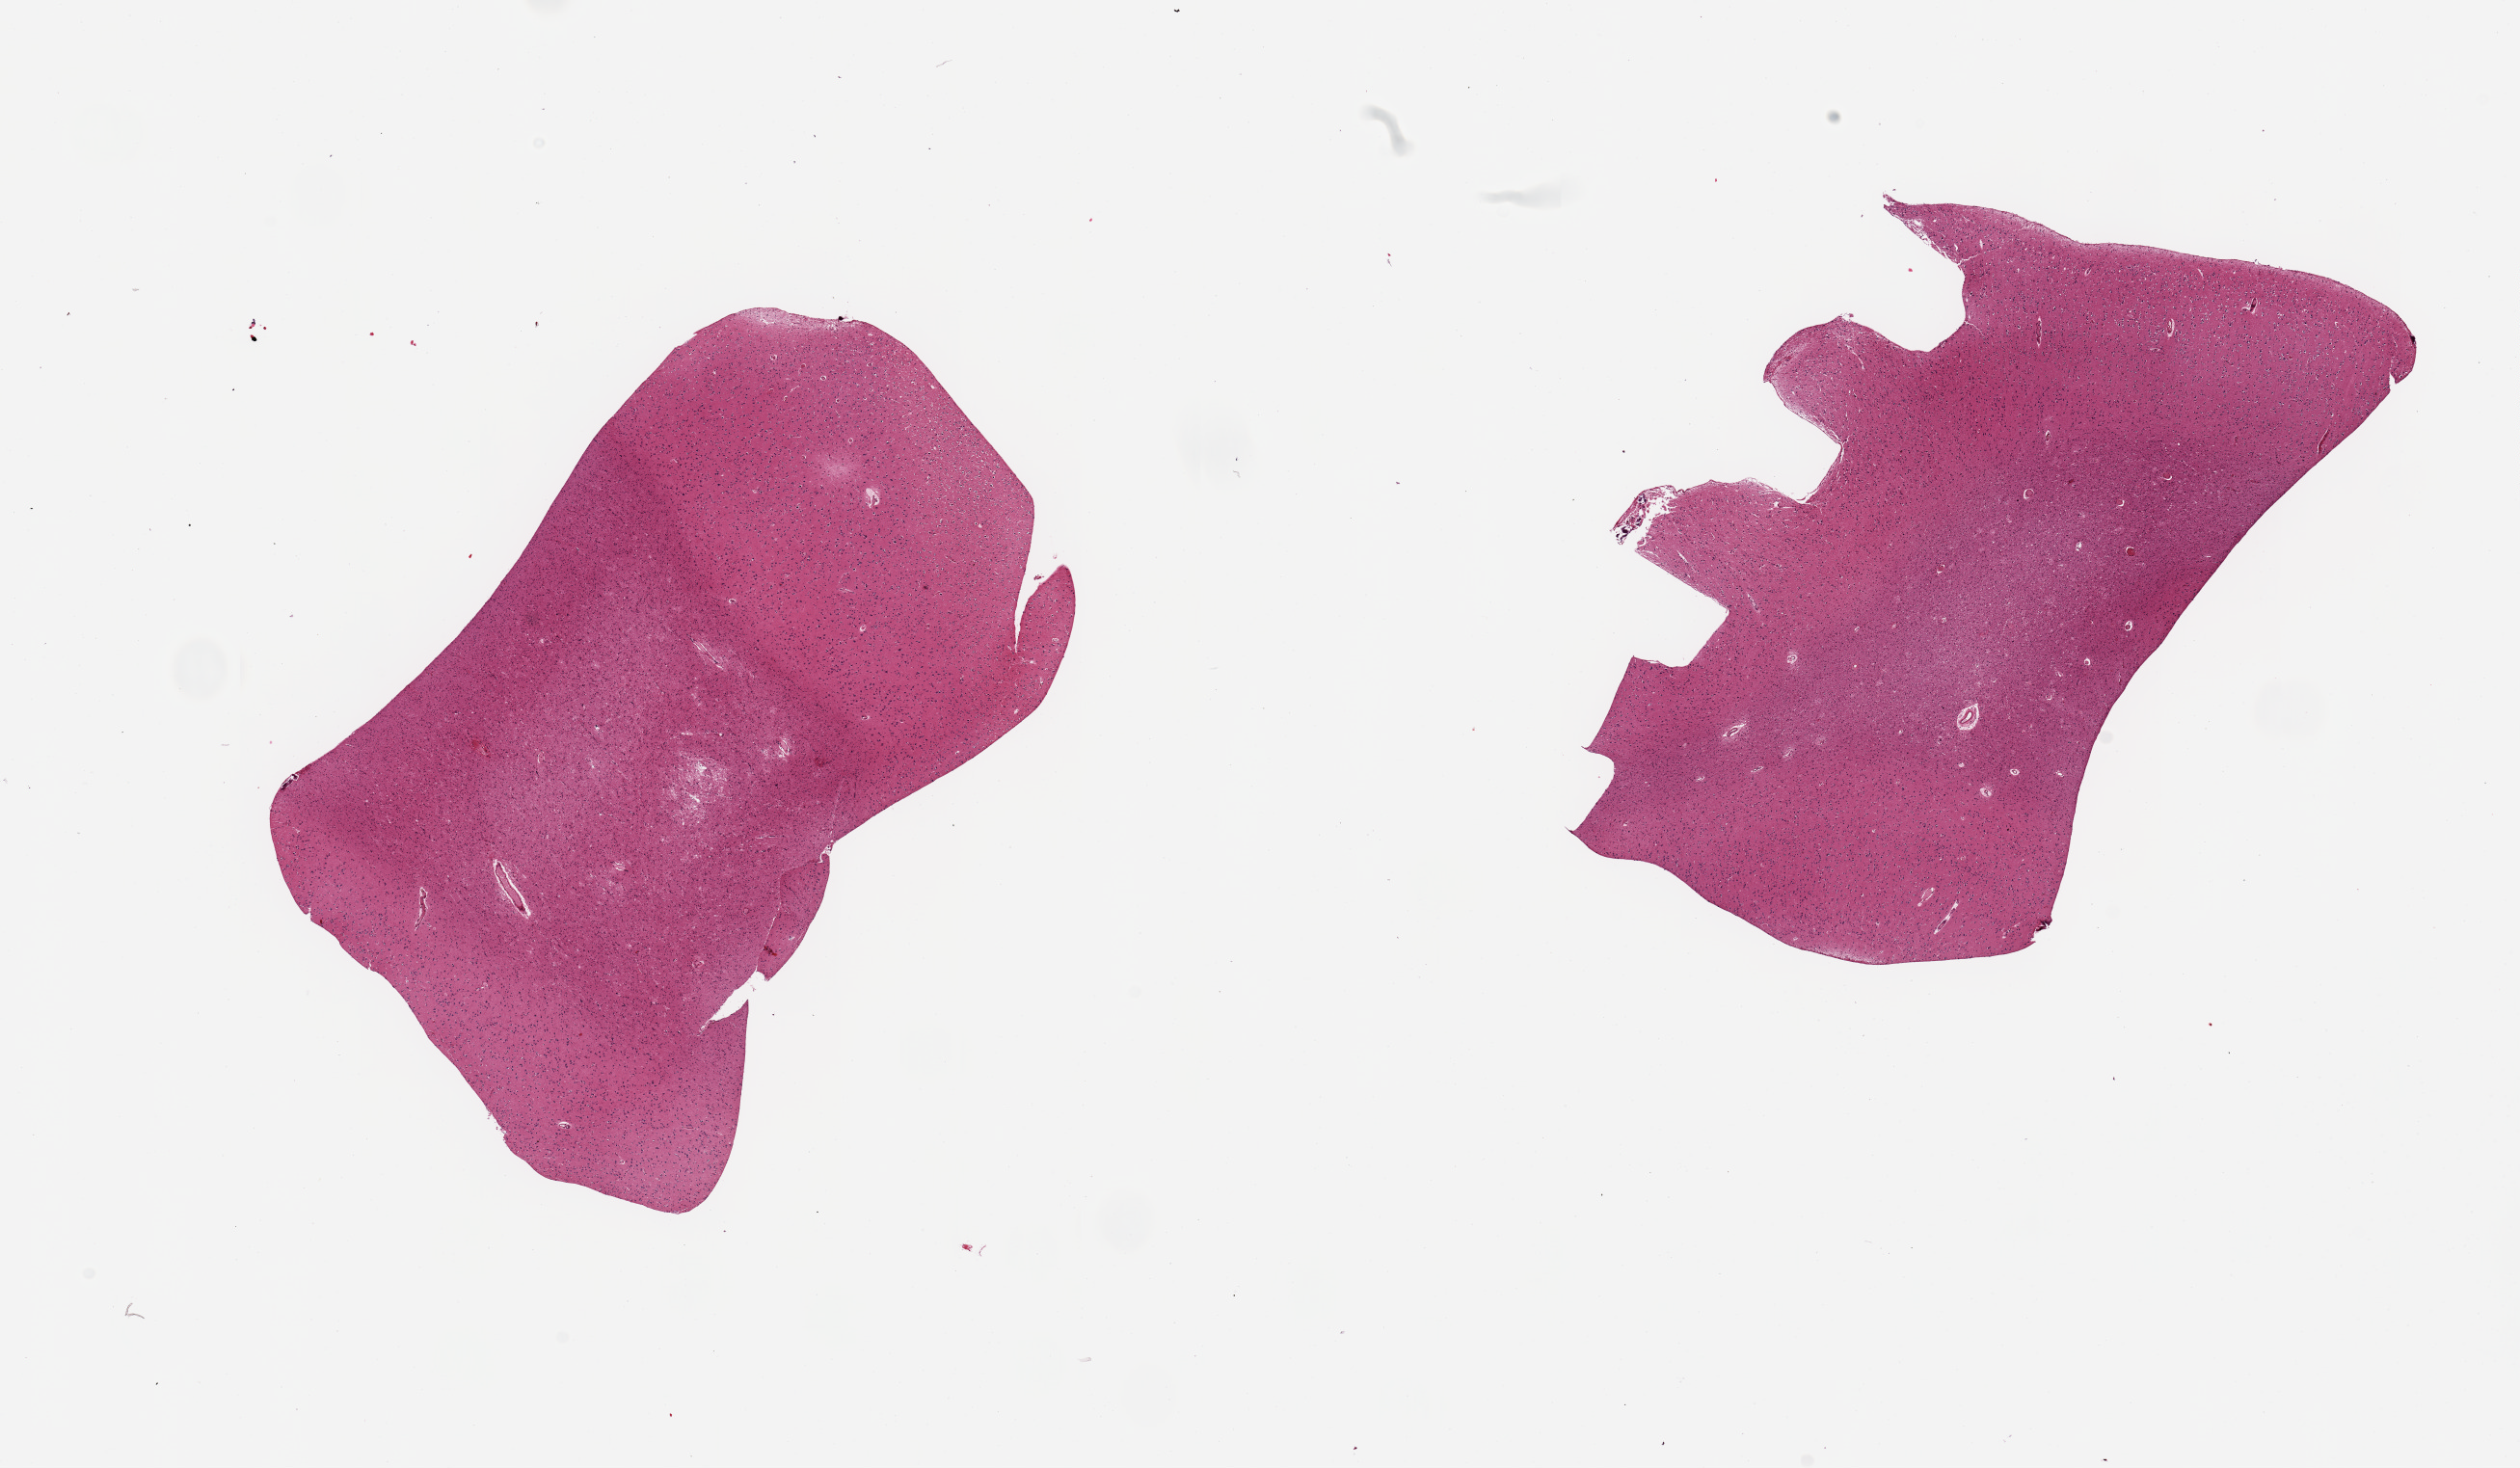
Digitized H&E-stained section, brightfield — a low-resolution overview of the entire scanned area, about 20.7 x 12.0 mm (acquisition: 20x scan). PAXgene-fixed paraffin-embedded (PFPE) section. Section of cerebral cortex (target tissue). Donor tissue sample.
* review note (as recorded): 2 pieces